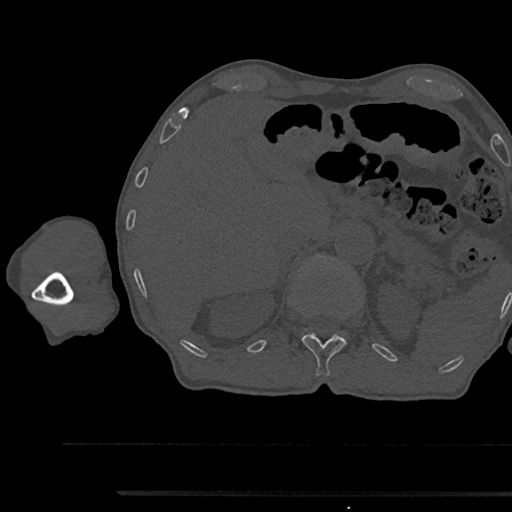
CT including the spine, one axial slice; slice 690 of 797 in the series (ordered by position); 120 kVp; bone window (W 1800 / L 400 HU); 0.5 mm slice thickness; 512 × 512 image matrix. Male patient, age 79 years. From the clinical record (not read from this slice): primary cancer: prostate.
Outlined on this slice (semi-automatically segmented with operator editing):
- L1 vertebra: bounding box (x1, y1, x2, y2) in pixels: (314, 254, 346, 339)
- T12 vertebra: (302, 333, 347, 377)